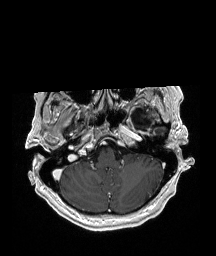
Brain MRI from a brain-tumour surgery series, one axial slice; T1-weighted post-contrast; 216 × 256 image matrix, field of view 211 × 250 mm. Case-level facts recorded for this patient, not image findings: histopathology: Glioblastoma; WHO grade: 4; IDH mutation: no.
Annotated regions visible in this slice (manually delineated by an expert):
- previous resection cavity: bounding box (x1, y1, x2, y2) in pixels: (128, 108, 154, 132)